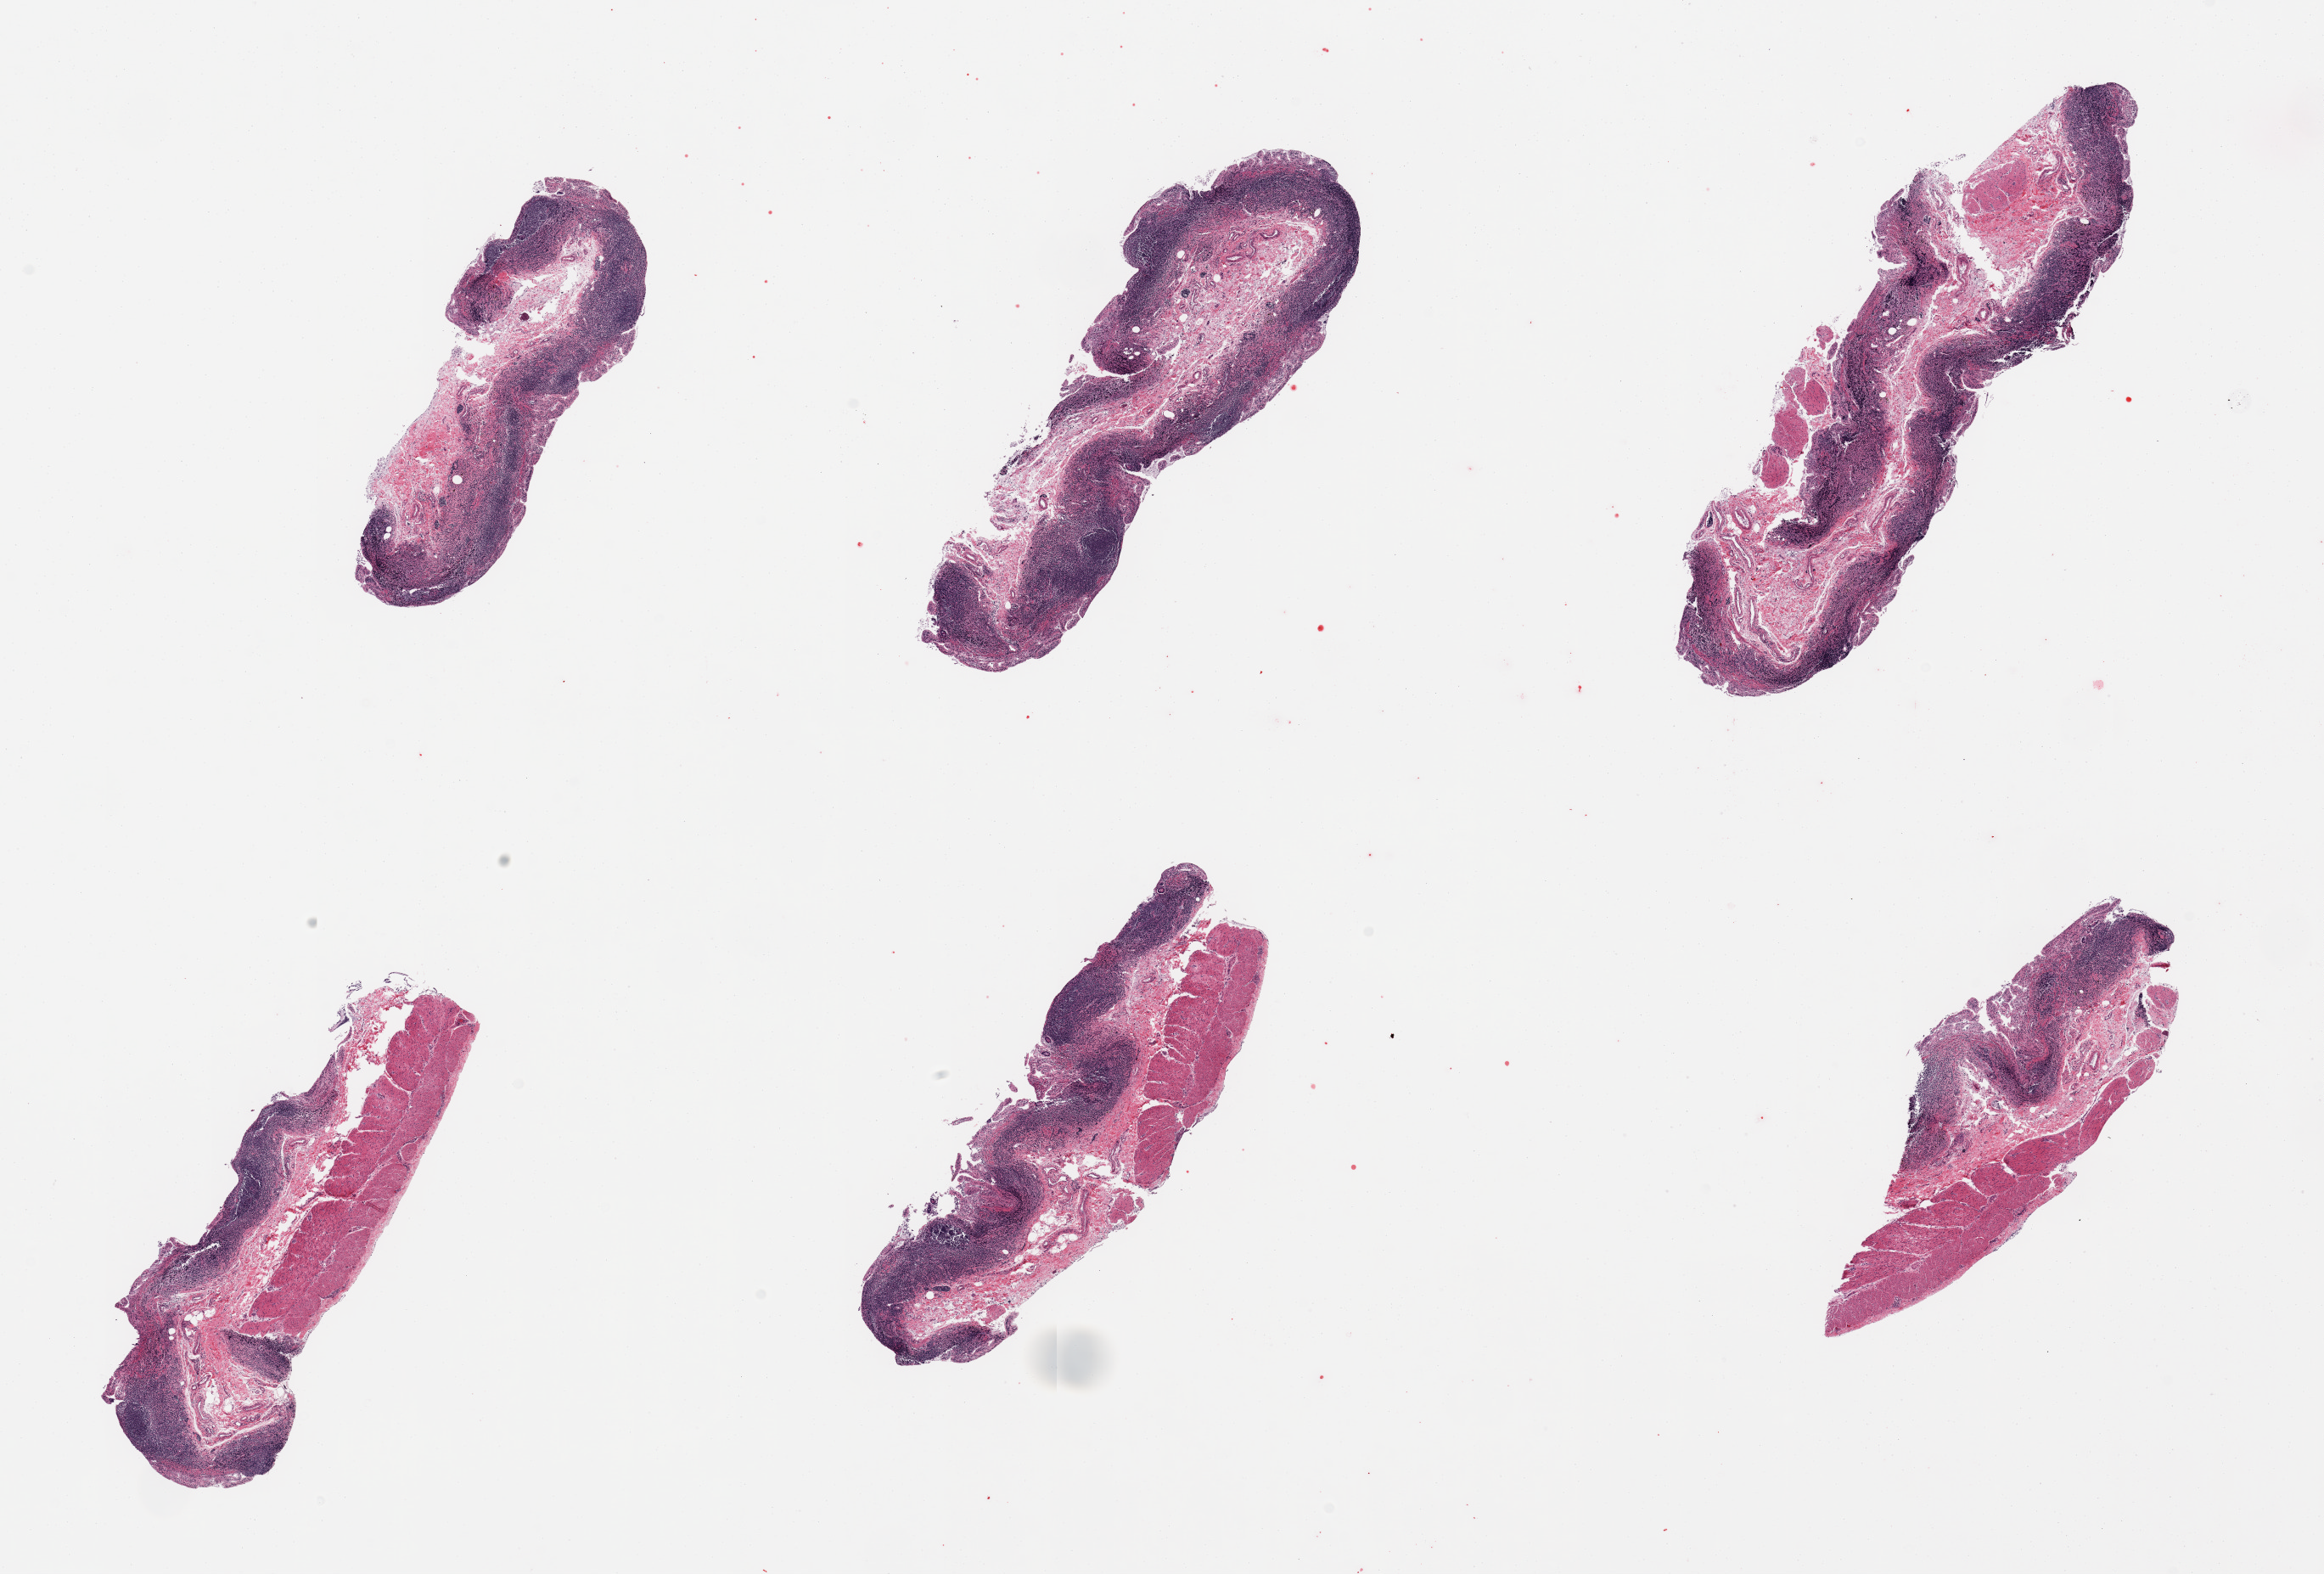
Digitized H&E-stained section, brightfield — low-resolution overview of the scanned area, about 21.7 x 14.7 mm. PAXgene-fixed paraffin-embedded (PFPE) section. Sampled site (target tissue): ileum. Tissue donor sample. Donor: female.
• review note (as recorded): 6 pieces; autolyzed mucosa and abundant lymphoid component, several pieces include significant muscularis (not target)